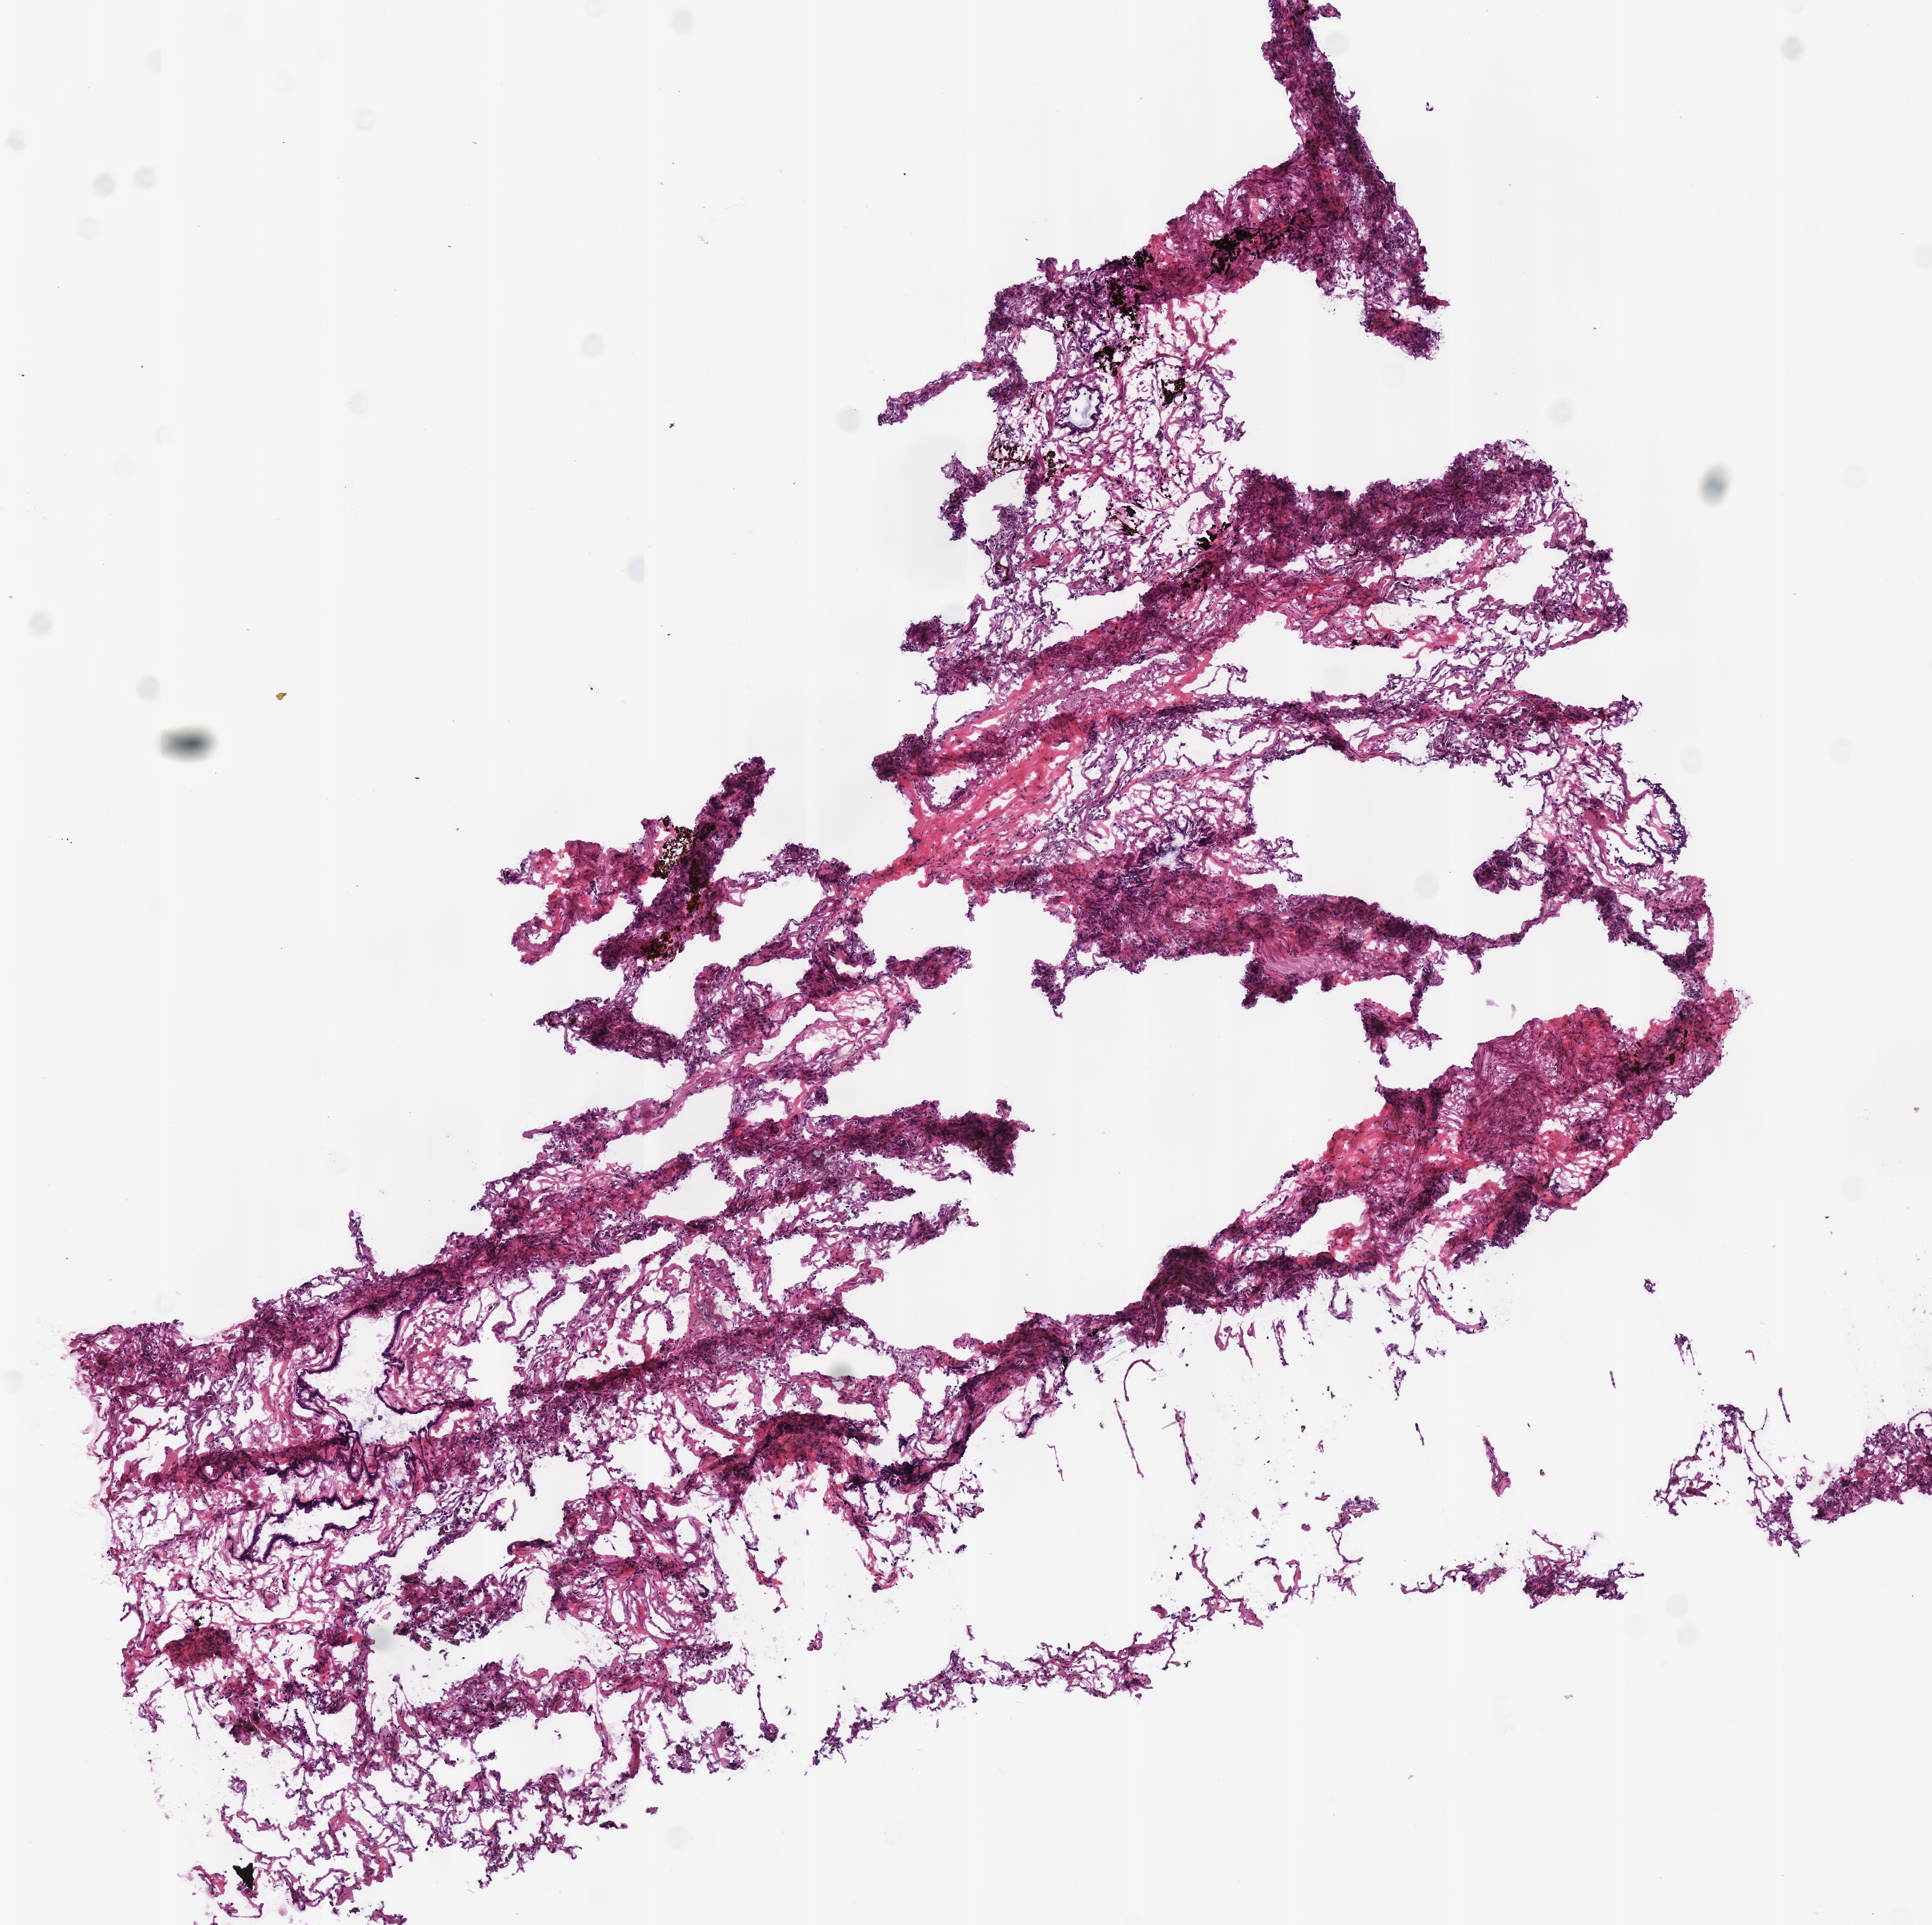
Whole-slide histology image, H&E-stained — shown as a low-resolution overview of the whole scanned area (about 5.9 x 5.9 mm). Frozen section. Sample: solid tissue normal (non-tumour tissue), lung. Patient: male, age at initial diagnosis 73 years.
This section: solid tissue normal (non-tumour) sample from the same patient. Patient diagnosis: Squamous cell carcinoma, NOS.